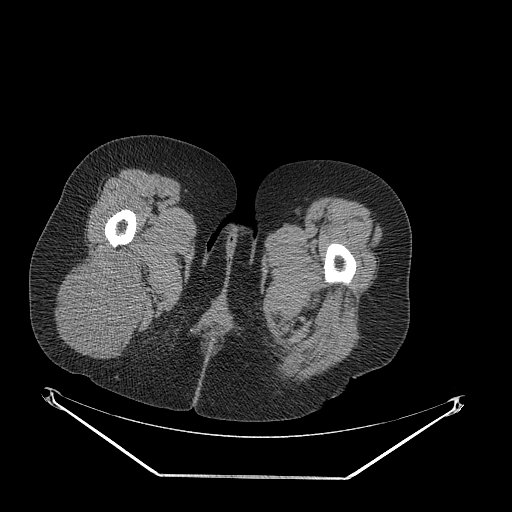
CT of an extremity soft-tissue mass (from a PET/CT study), one axial slice; position 47 of 257 along the scan axis; reconstruction kernel STANDARD; 140 kVp; soft-tissue window (W 400 / L 40 HU); 3.75 mm slice thickness; 512 × 512 image matrix, field of view 500 × 500 mm. Female patient. Case-level facts recorded for this patient, not image findings: histological type: synovial sarcoma; grade: intermediate; site of the primary tumour: right buttock.
Structures marked on this image (expert contour drawn on MRI and transferred to this co-registered scan by the dataset authors):
- gross tumour volume including surrounding oedema: box from (x=64, y=249) to (x=147, y=350) px
- gross tumour volume (mass): (x=64, y=249)–(x=147, y=350)